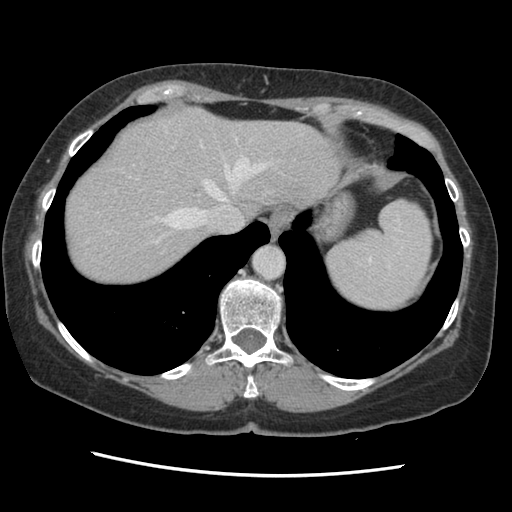
Contrast-enhanced abdominal CT, one axial slice. Position 115 of 141 along the scan axis. 120 kVp. Soft-tissue window (W 400 / L 40 HU). 2.5 mm slice thickness. 512 × 512 image matrix. Female patient, age 61 years. Case-level facts recorded for this patient, not image findings: diagnosis: colorectal cancer liver metastases, imaged before liver resection; multiple liver metastases: no; largest metastasis: 2.4 cm; disease in both lobes: no.
Outlined on this slice (expert manual segmentation):
- hepatic veins: bounding box (x1, y1, x2, y2) in pixels: (133, 126, 271, 244)
- liver: (64, 106, 340, 286)
- planned liver remnant (the part of the liver to remain after resection): (64, 106, 340, 286)